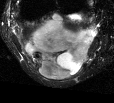
MRI of an extremity soft-tissue mass, one axial slice; slice 20 of 44 in the series (ordered by position); T2-weighted fat-saturated; MR volume resampled by the dataset authors to the PET/CT grid (not the native acquisition matrix); 3.27 mm slice thickness; 114 × 103 image matrix. Female patient. Case-level facts recorded for this patient, not image findings: histological type: liposarcoma; site of the primary tumour: right thigh.
Annotated regions visible in this slice (expert contour drawn on MRI and transferred to this co-registered scan by the dataset authors):
- gross tumour volume (mass): bounding box (x1, y1, x2, y2) in pixels: (24, 14, 98, 79)